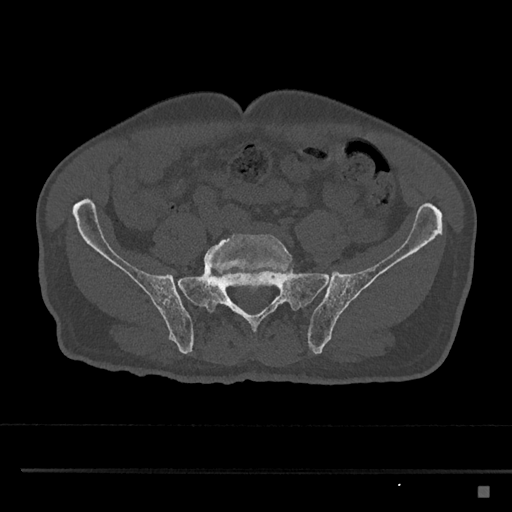
CT including the spine, one axial slice; position 551 of 797 along the scan axis; bone window (W 1800 / L 400 HU); 512 × 512 image matrix, field of view 391 × 391 mm. Patient: male, 59 years. From the clinical record (not read from this slice): primary cancer: prostate.
Structures marked on this image (semi-automatic segmentation, software-assisted and operator-edited):
- L5 vertebra: bounding box <204,233,292,277> (left, top, right, bottom; pixels)